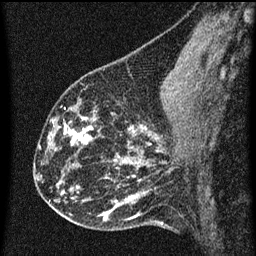
Breast MRI (dynamic contrast-enhanced), one sagittal slice; position 24 of 60 along the scan axis; dynamic contrast-enhanced series, image 2 of 3 at this slice position (ordered by acquisition); 1.5 T; TE 4.2 ms, TR 8 ms; 2 mm slice thickness; 256 × 256 image matrix. Patient: female, 43 years.
Structures marked on this image (semi-automatic segmentation, software-assisted and operator-edited):
- analysis volume of interest (the breast-tissue region the enhancement analysis was run in; not a lesion): box from (x=55, y=104) to (x=102, y=153) px
- tumour enhancement mask (voxels above the 70 % enhancement threshold inside the analysis volume of interest): (x=65, y=118)–(x=93, y=145)